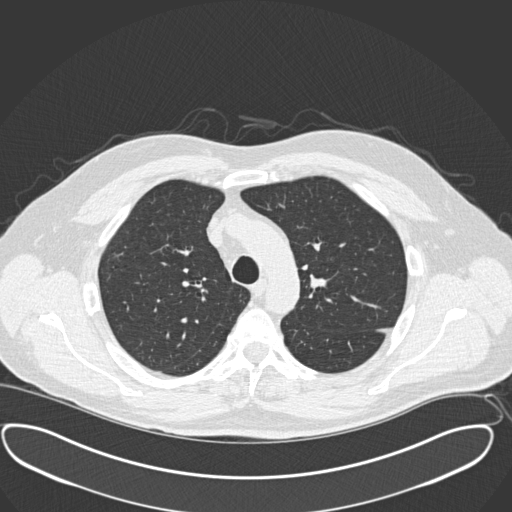
Chest CT (low-dose screening protocol), one axial image; third annual screen; lung window (W 1500 / L -600 HU); 2 mm slice thickness; 512 × 512 image matrix. Male participant, aged 56 years at enrolment.
- Expert reader's lesion annotation, bounding box (x1, y1, x2, y2) in pixels: (286, 262, 345, 311).
- No non-calcified nodule or mass ≥4 mm was recorded by the screening reader at this exam.
- Official screen result: negative screen, minor abnormalities not suspicious for lung cancer.
- Participant outcome: lung cancer diagnosed 156 days after this screen — neuroendocrine carcinoma, NOS, left upper lobe, well differentiated (G1), stage IA (AJCC 6th edition), 20 mm at pathology.